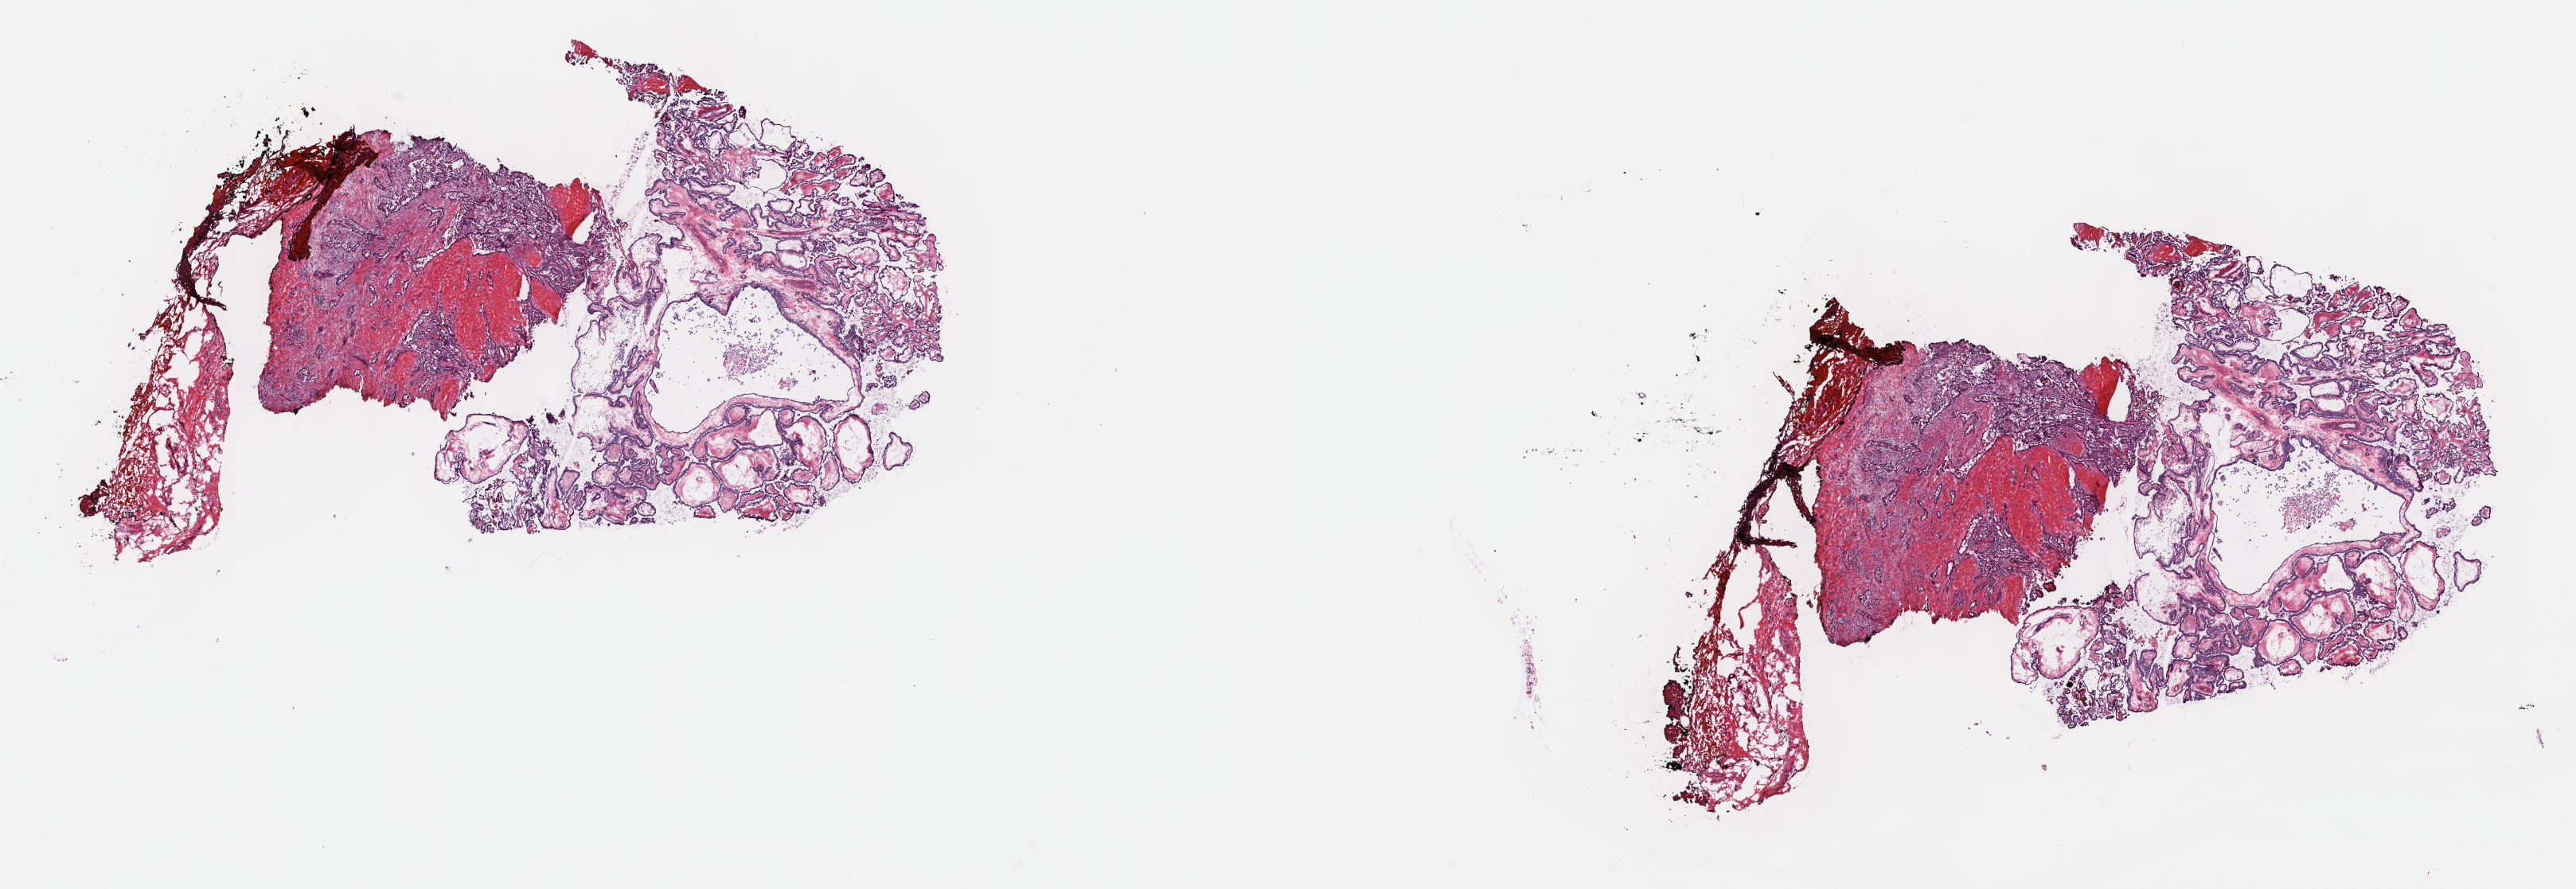
Whole-slide histology image, H&E, a low-resolution overview of the entire scanned area, about 26.2 x 9.0 mm (from a 40x scan), frozen section, thyroid, primary tumour sample. Female patient; age at initial diagnosis 36 years. Slide review estimates, as recorded: tumour cells 30%, tumour nuclei 95%, normal cells 0%, stromal cells 70%, necrosis 0%. Infiltration values recorded for this section: lymphocyte infiltration 3%, monocyte infiltration 3%, neutrophil infiltration 0%.
Laterality: right. AJCC pathologic stage: I. Pathologic diagnosis: Papillary adenocarcinoma, NOS (thyroid gland).